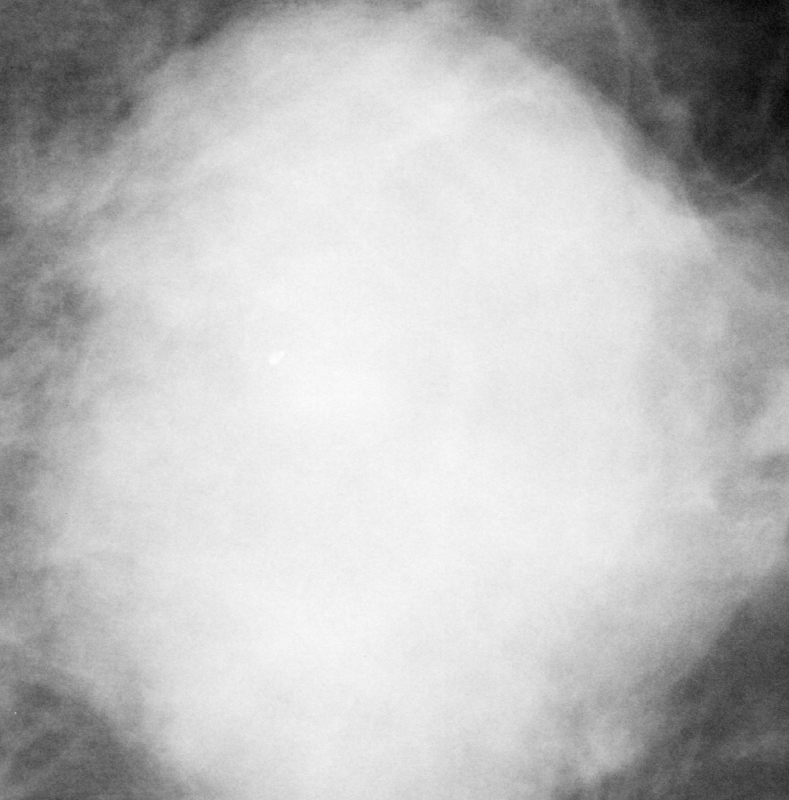
Cropped region of a digitized screen-film mammogram centred on a radiologist-marked abnormality, left breast, CC view.
Finding: mass, shape oval, margins microlobulated; BI-RADS assessment category 5; pathology (as recorded): malignant.